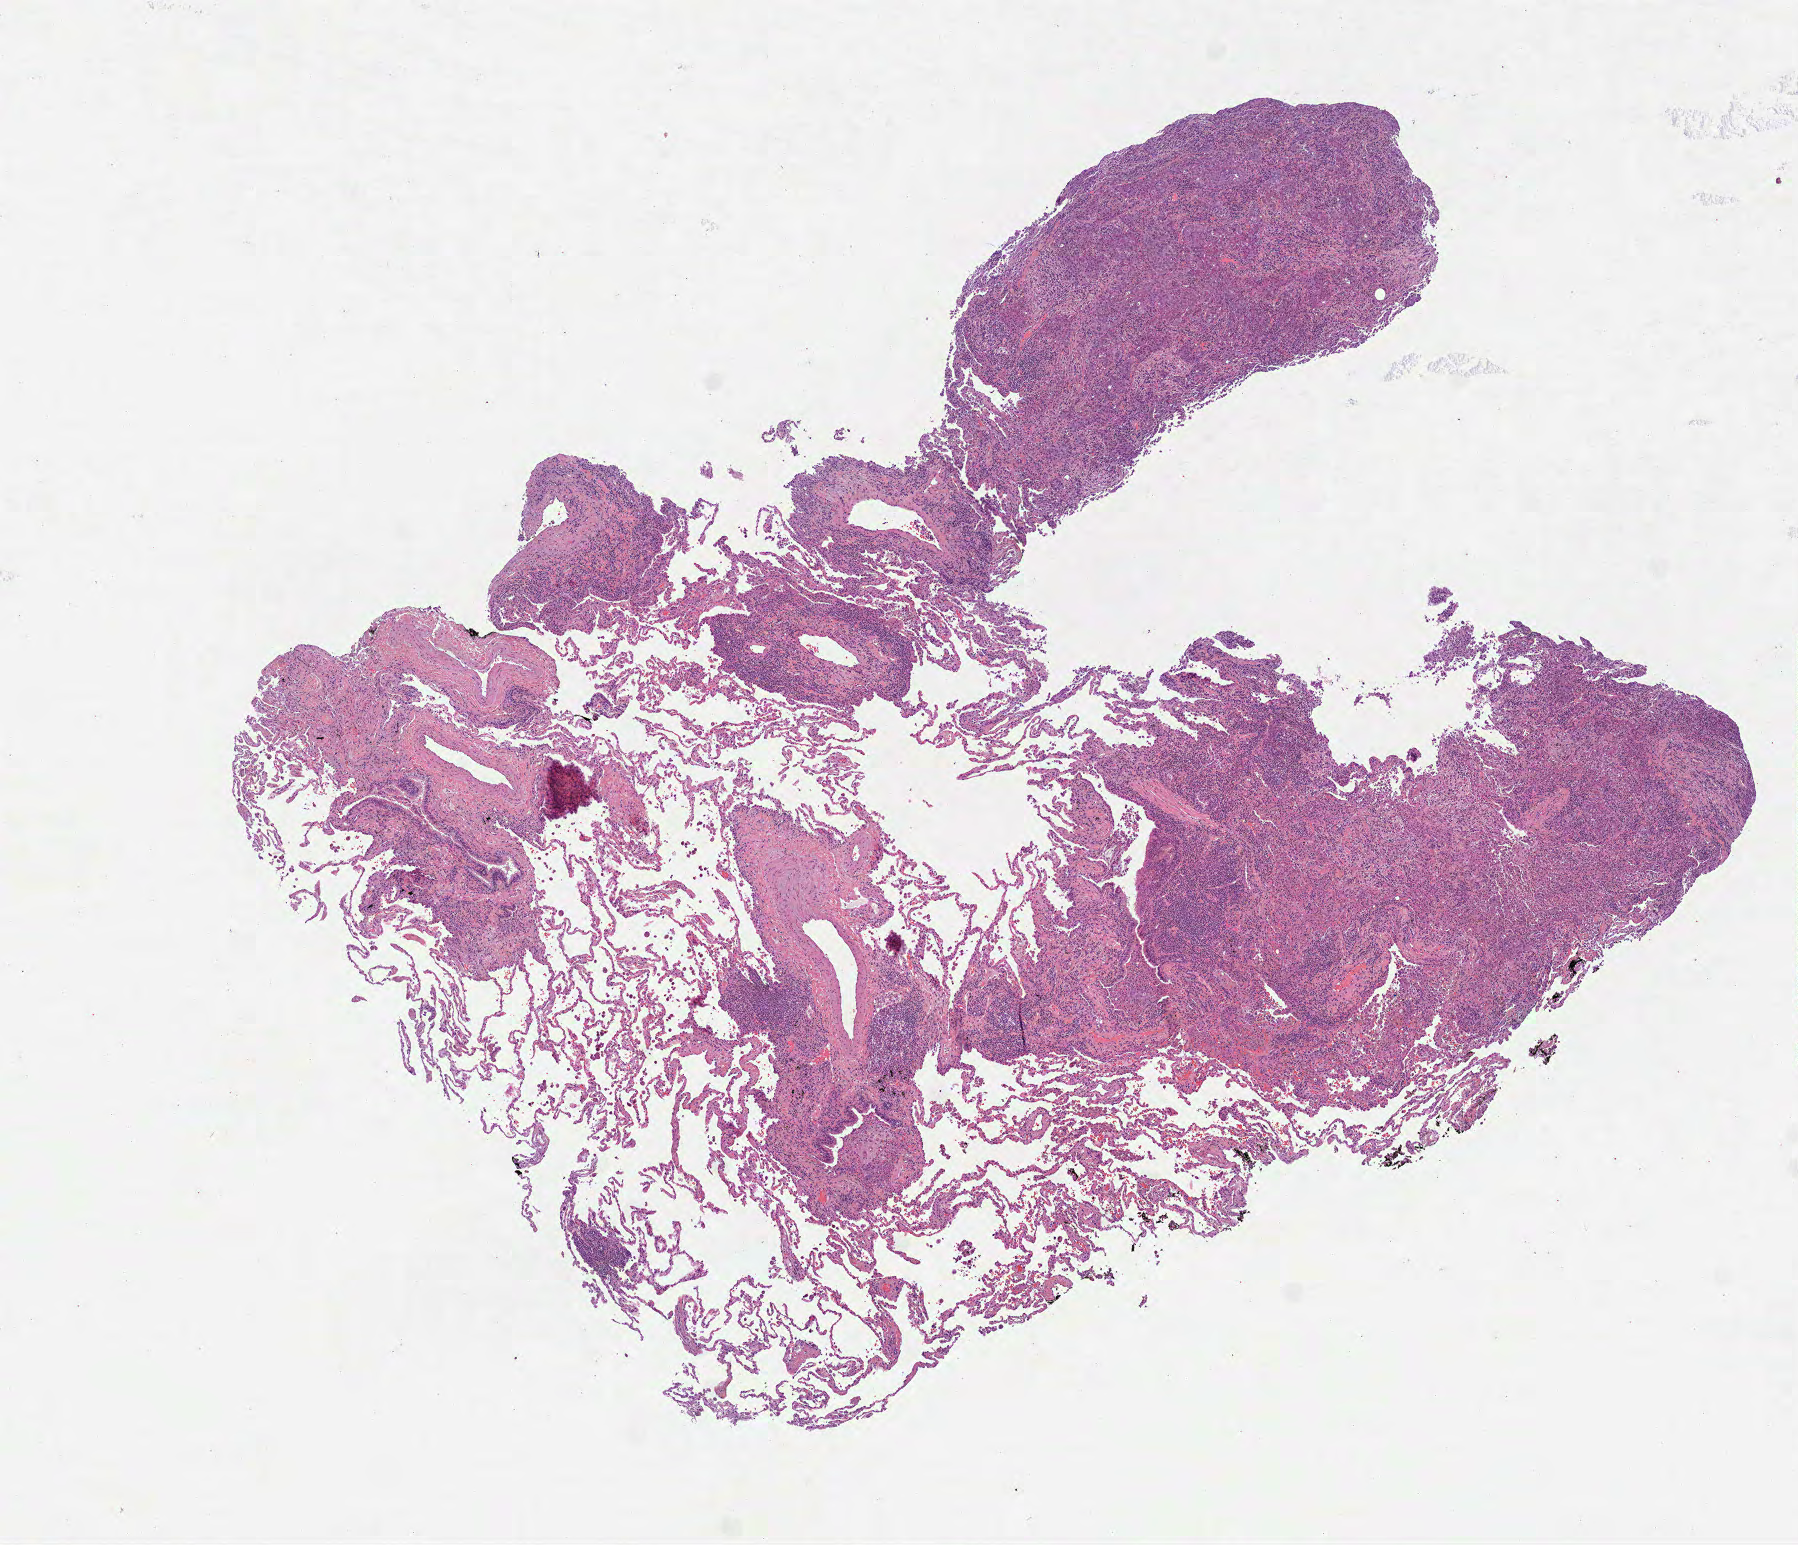
Whole-slide histology image, H&E-stained, whole scanned area (about 7.3 x 6.2 mm) shown as a low-resolution overview, formalin-fixed paraffin-embedded (FFPE) diagnostic section, primary tumour sample from the lung. Patient: male, age at initial diagnosis 77 years.
Histologic diagnosis: Adenocarcinoma, NOS. AJCC pathologic stage: IA (6th edition). TNM: T1 N0 M0.